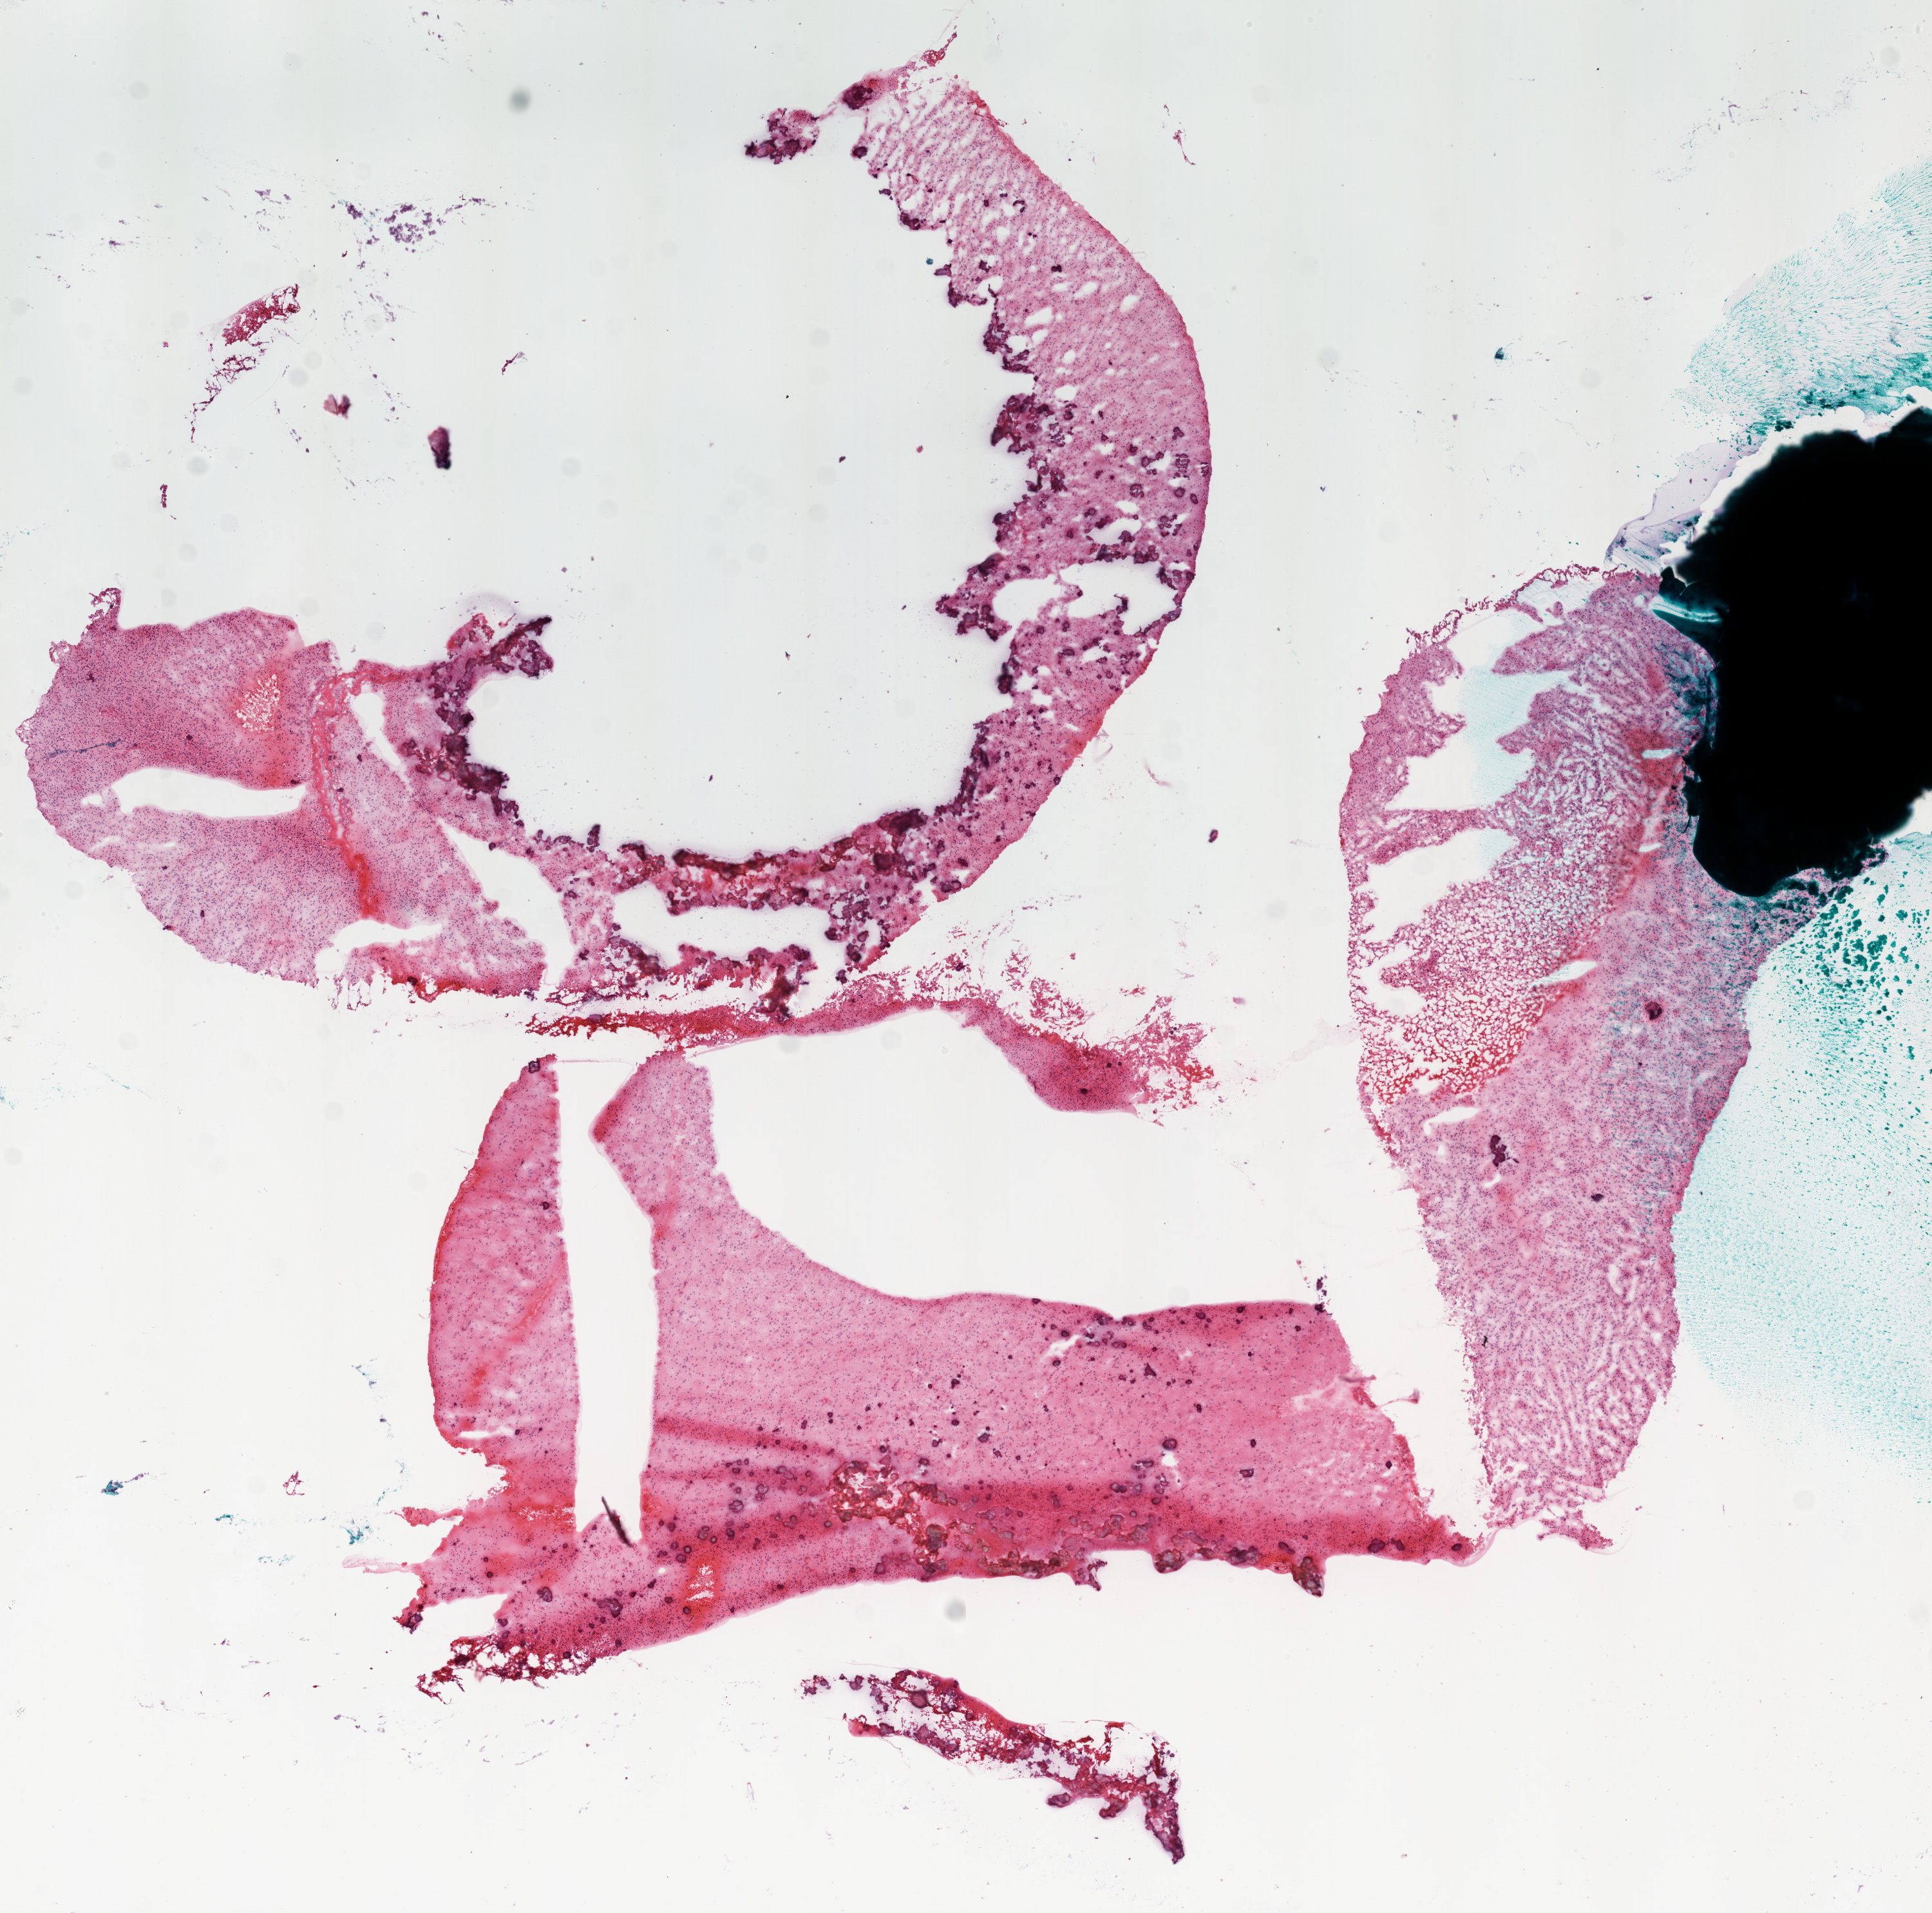
Whole-slide histology image, H&E-stained — low-resolution overview of the scanned area, about 12.0 x 11.9 mm; frozen section; brain, primary tumour sample. Male, age 54 years at initial diagnosis. Slide review estimates, as recorded: tumour cells 80%, tumour nuclei 95%, normal cells 0%, stromal cells 15%, necrosis 5%.
Histologic diagnosis: Glioblastoma.